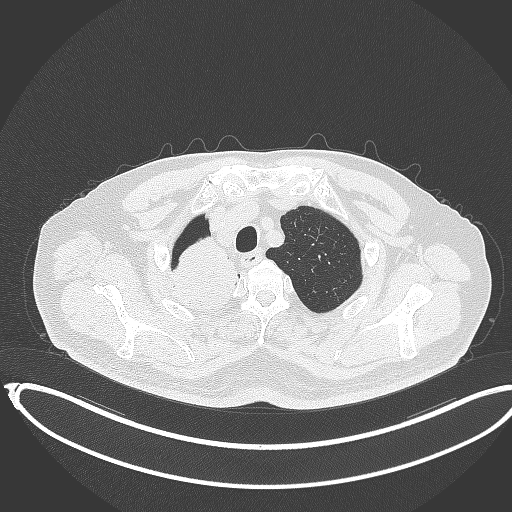
Chest CT, one axial slice; position 320 of 403 along the scan axis; reconstruction kernel B70f; 120 kVp; lung window (W 1500 / L -600 HU); 1 mm slice thickness; 512 × 512 image matrix, field of view 436 × 436 mm. Patient: male, 68 years. From the clinical record (not read from this slice): clinical TNM (as recorded): T2a N0 M0.
Annotated regions visible in this slice (rectangle marked by the reading radiologist):
- lung tumour (recorded histology: adenocarcinoma): bounding box <162,234,246,315> (left, top, right, bottom; pixels)